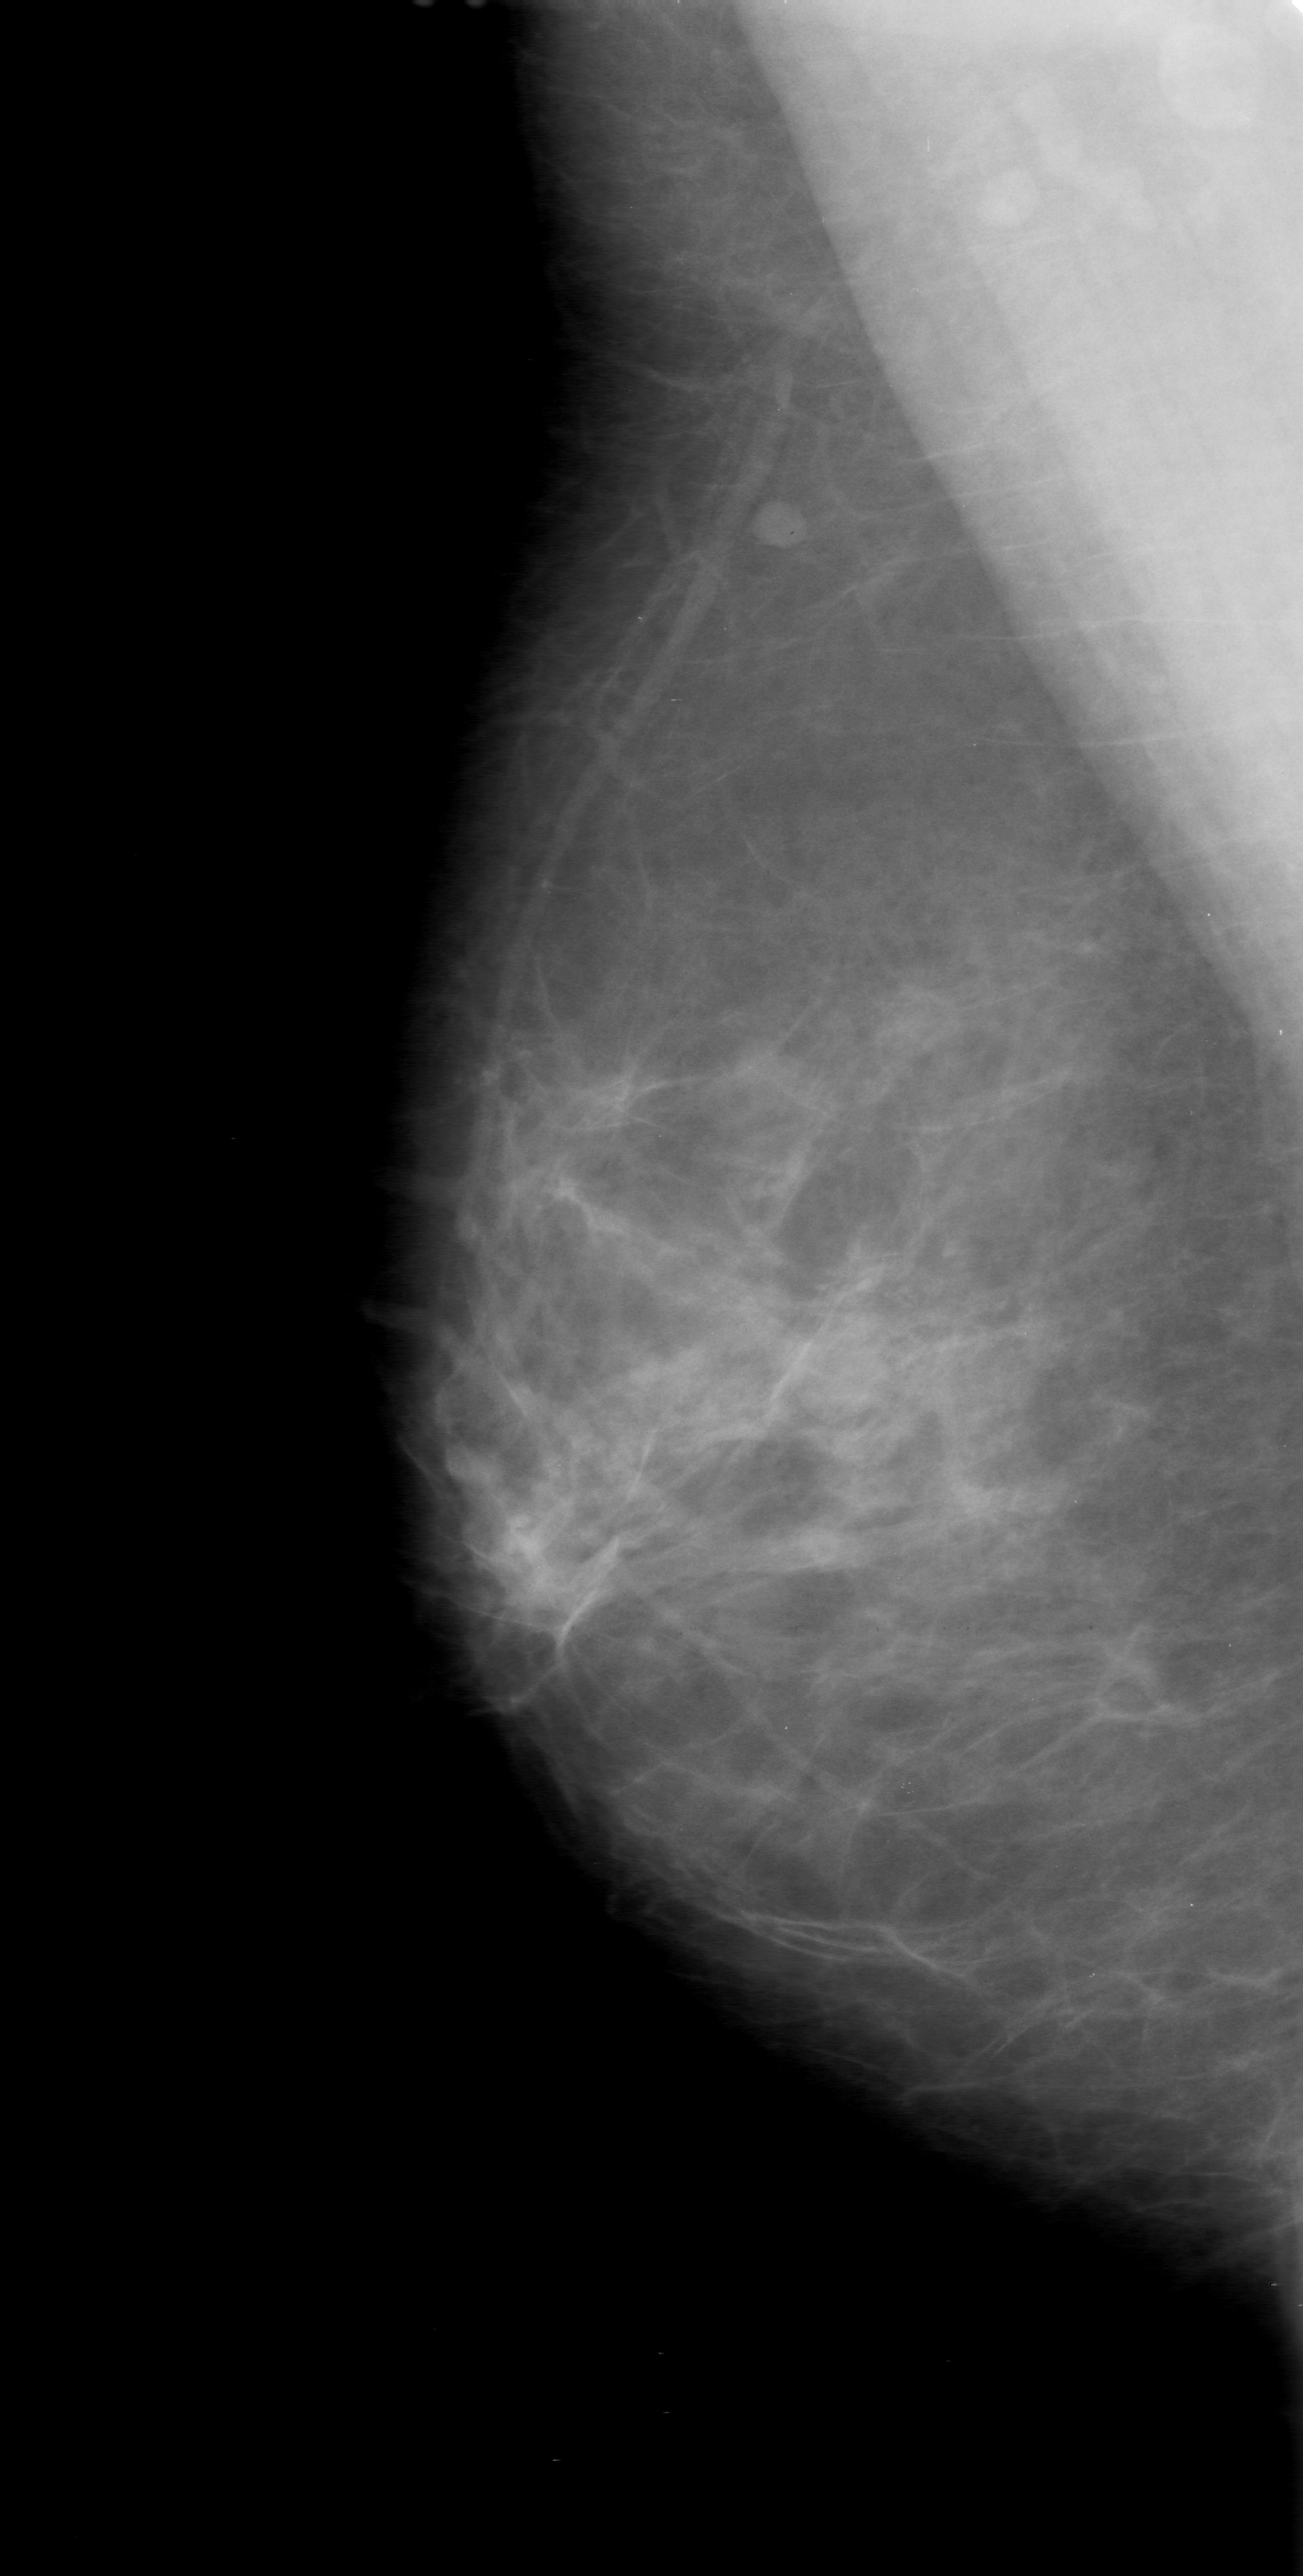
Digitized screen-film mammogram, right breast, mediolateral oblique (MLO) view, breast composition: scattered fibroglandular densities (BI-RADS density category 2 of 4).
Marked abnormality: mass, shape oval, margins obscured; BI-RADS assessment category 0 (incomplete: needs additional imaging); subtlety rating 3 on a 1 (subtle) to 5 (obvious) scale; pathology (as recorded): benign.